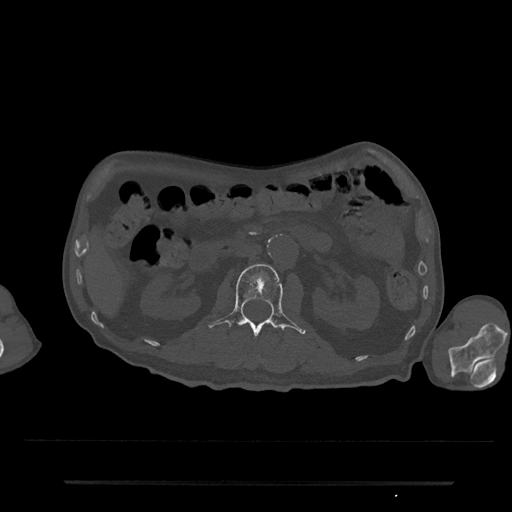
CT including the spine, one axial slice; slice 70 of 797 in the series (ordered by position); 120 kVp; bone window (W 1800 / L 400 HU); 0.5 mm slice thickness; 512 × 512 image matrix, field of view 427 × 427 mm. Patient: male, 74 years. Case-level facts recorded for this patient, not image findings: primary cancer: prostate.
Structures marked on this image (semi-automatic segmentation, software-assisted and operator-edited):
- L2 vertebra: box from (x=208, y=264) to (x=306, y=337) px